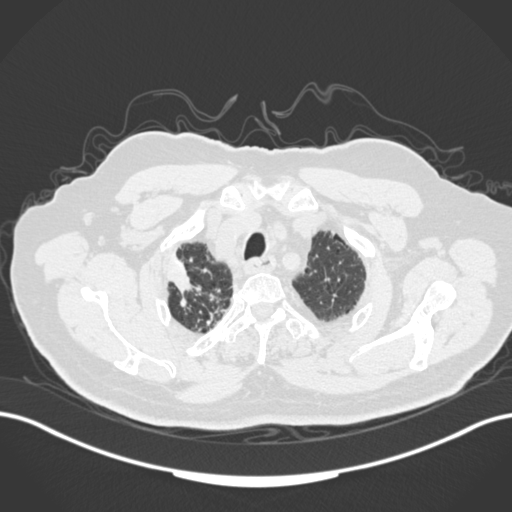
Chest CT, one axial slice. Position 150 of 205 along the scan axis. Reconstruction kernel B30f. 120 kVp. Lung window (W 1500 / L -600 HU). 512 × 512 image matrix, field of view 400 × 400 mm. Male patient, age 72 years. Case-level facts recorded for this patient, not image findings: clinical TNM (as recorded): T1a N0 M0.
Annotated regions visible in this slice (rectangle marked by the reading radiologist):
- lung tumour (recorded histology: squamous cell carcinoma): bounding box <163,254,197,294> (left, top, right, bottom; pixels)